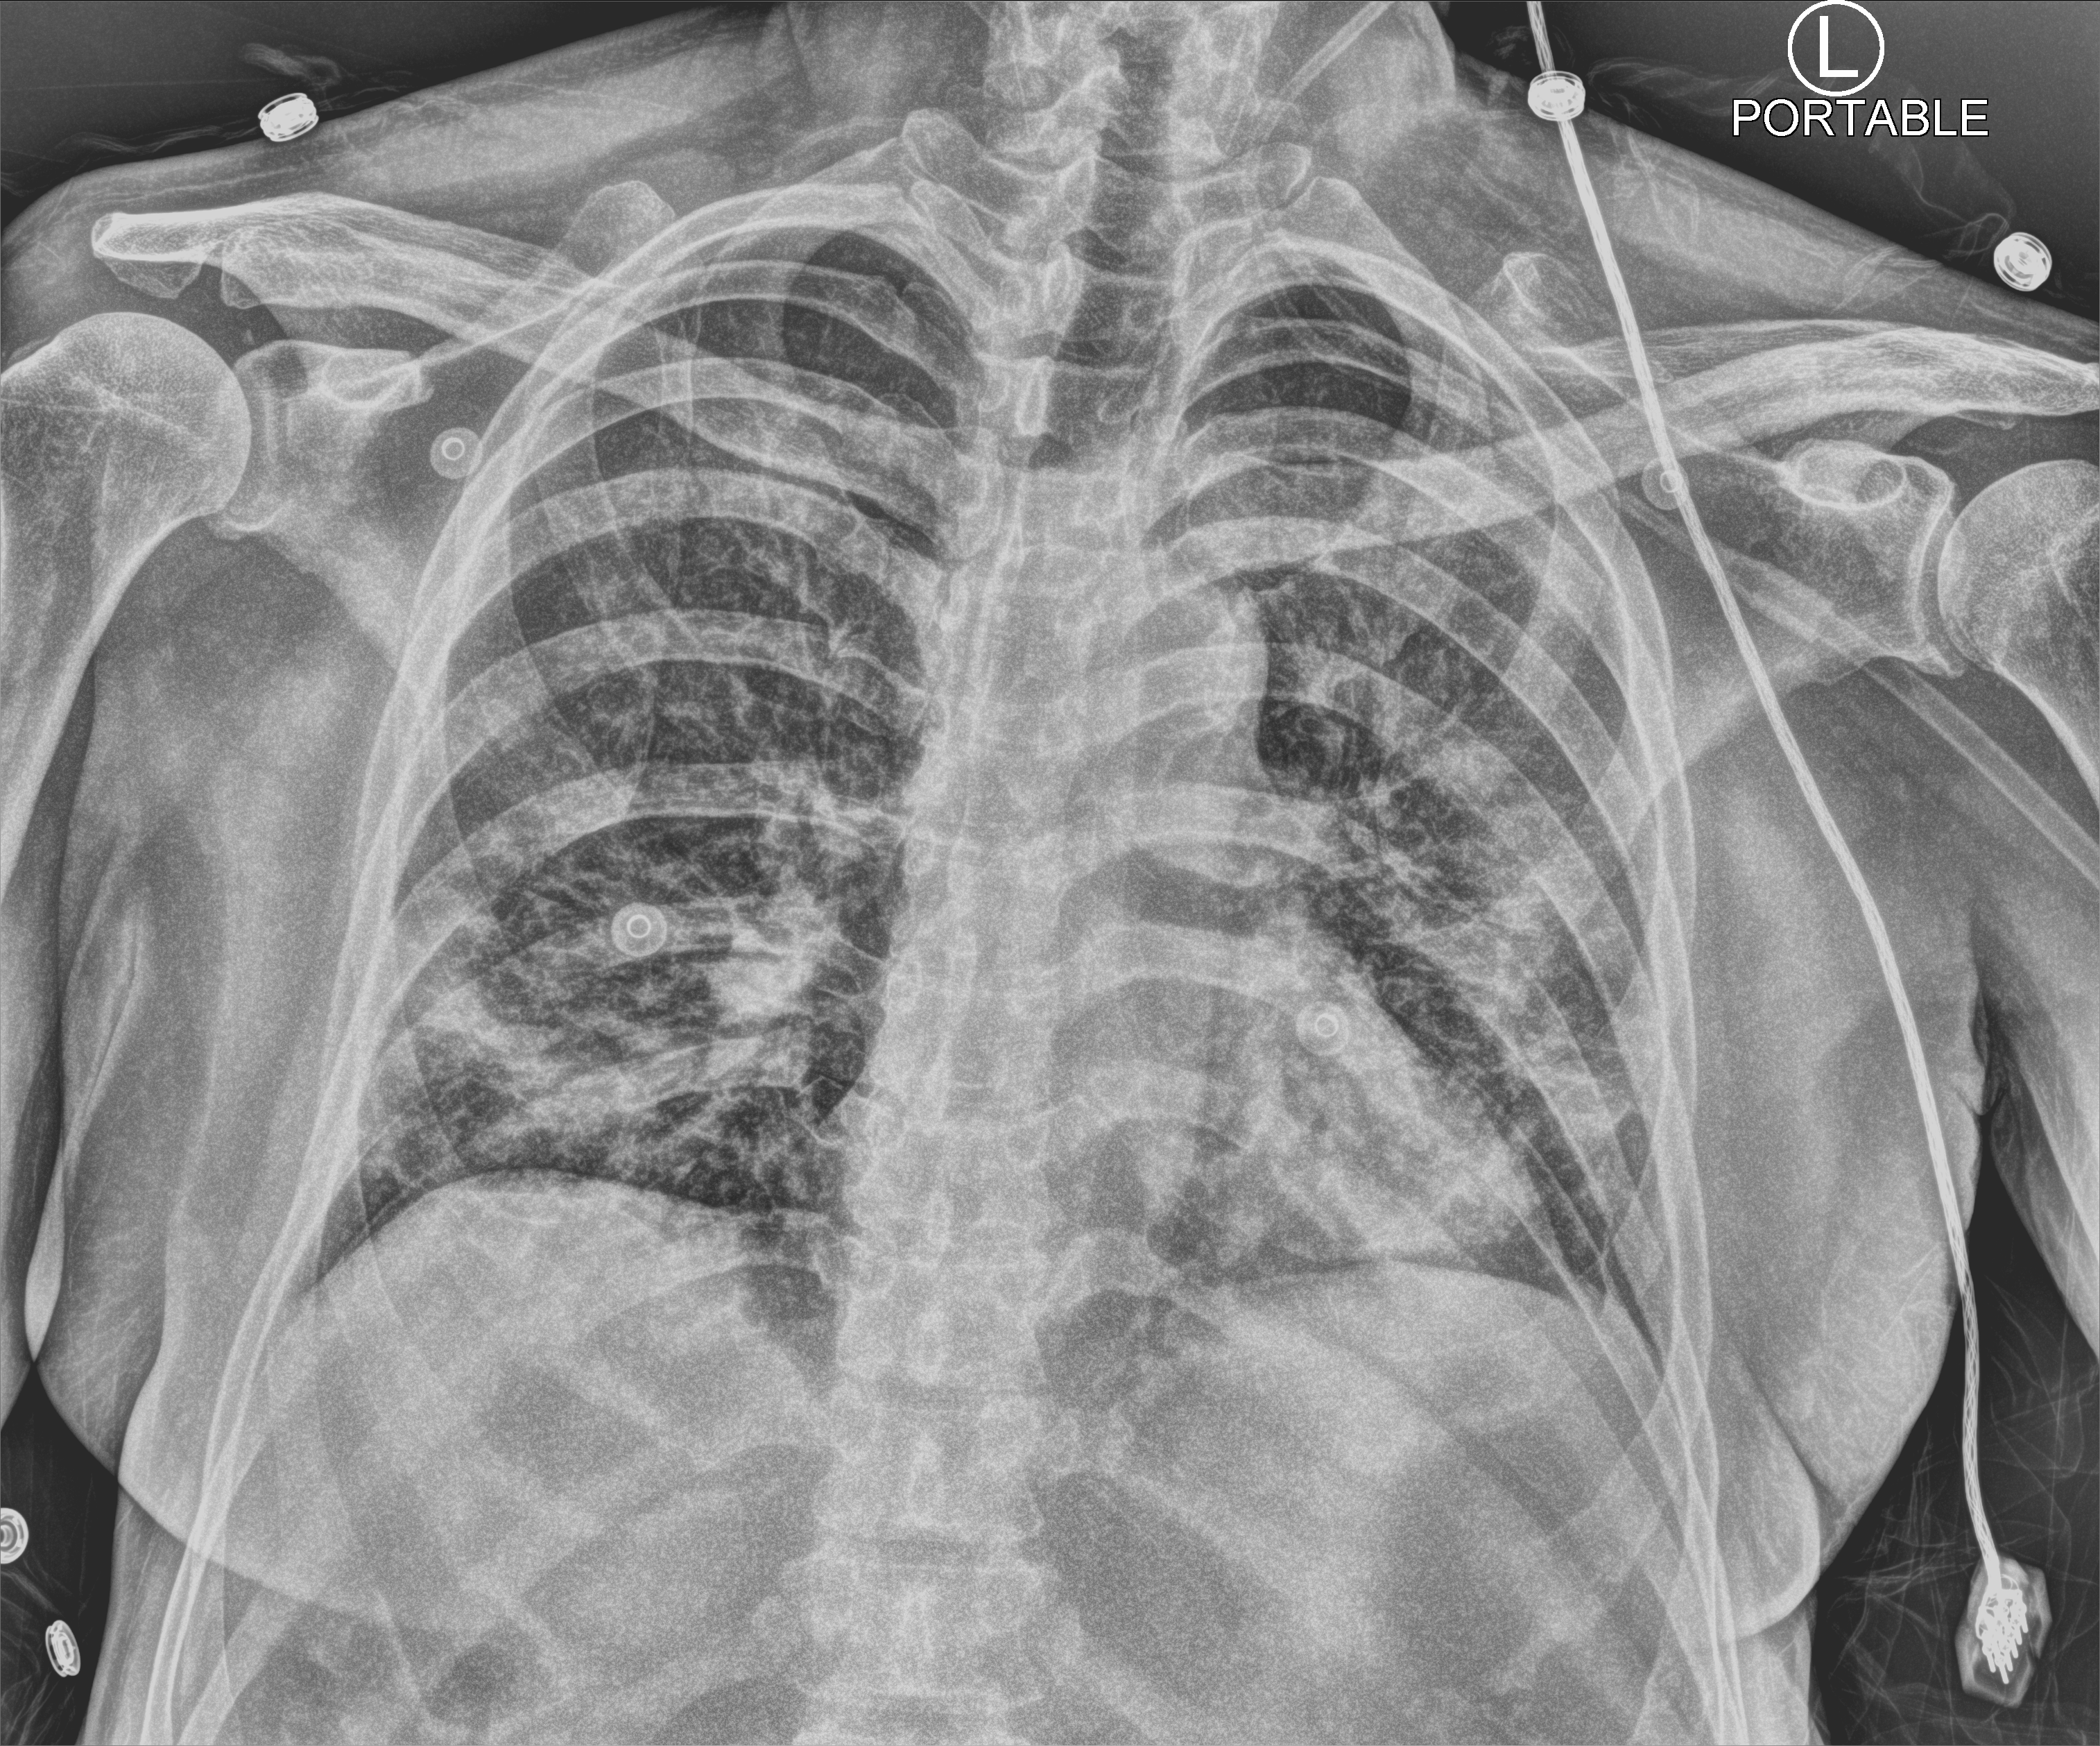
Chest X-ray (portable). Male patient hospitalised with COVID-19, age 60–74 years.
Hospital-stay facts (about this admission, not read from this image; timing relative to this image not recorded):
- admitted to intensive care during this hospital stay: no
- mechanically ventilated during this hospital stay: no
- smoking status (admission record): never